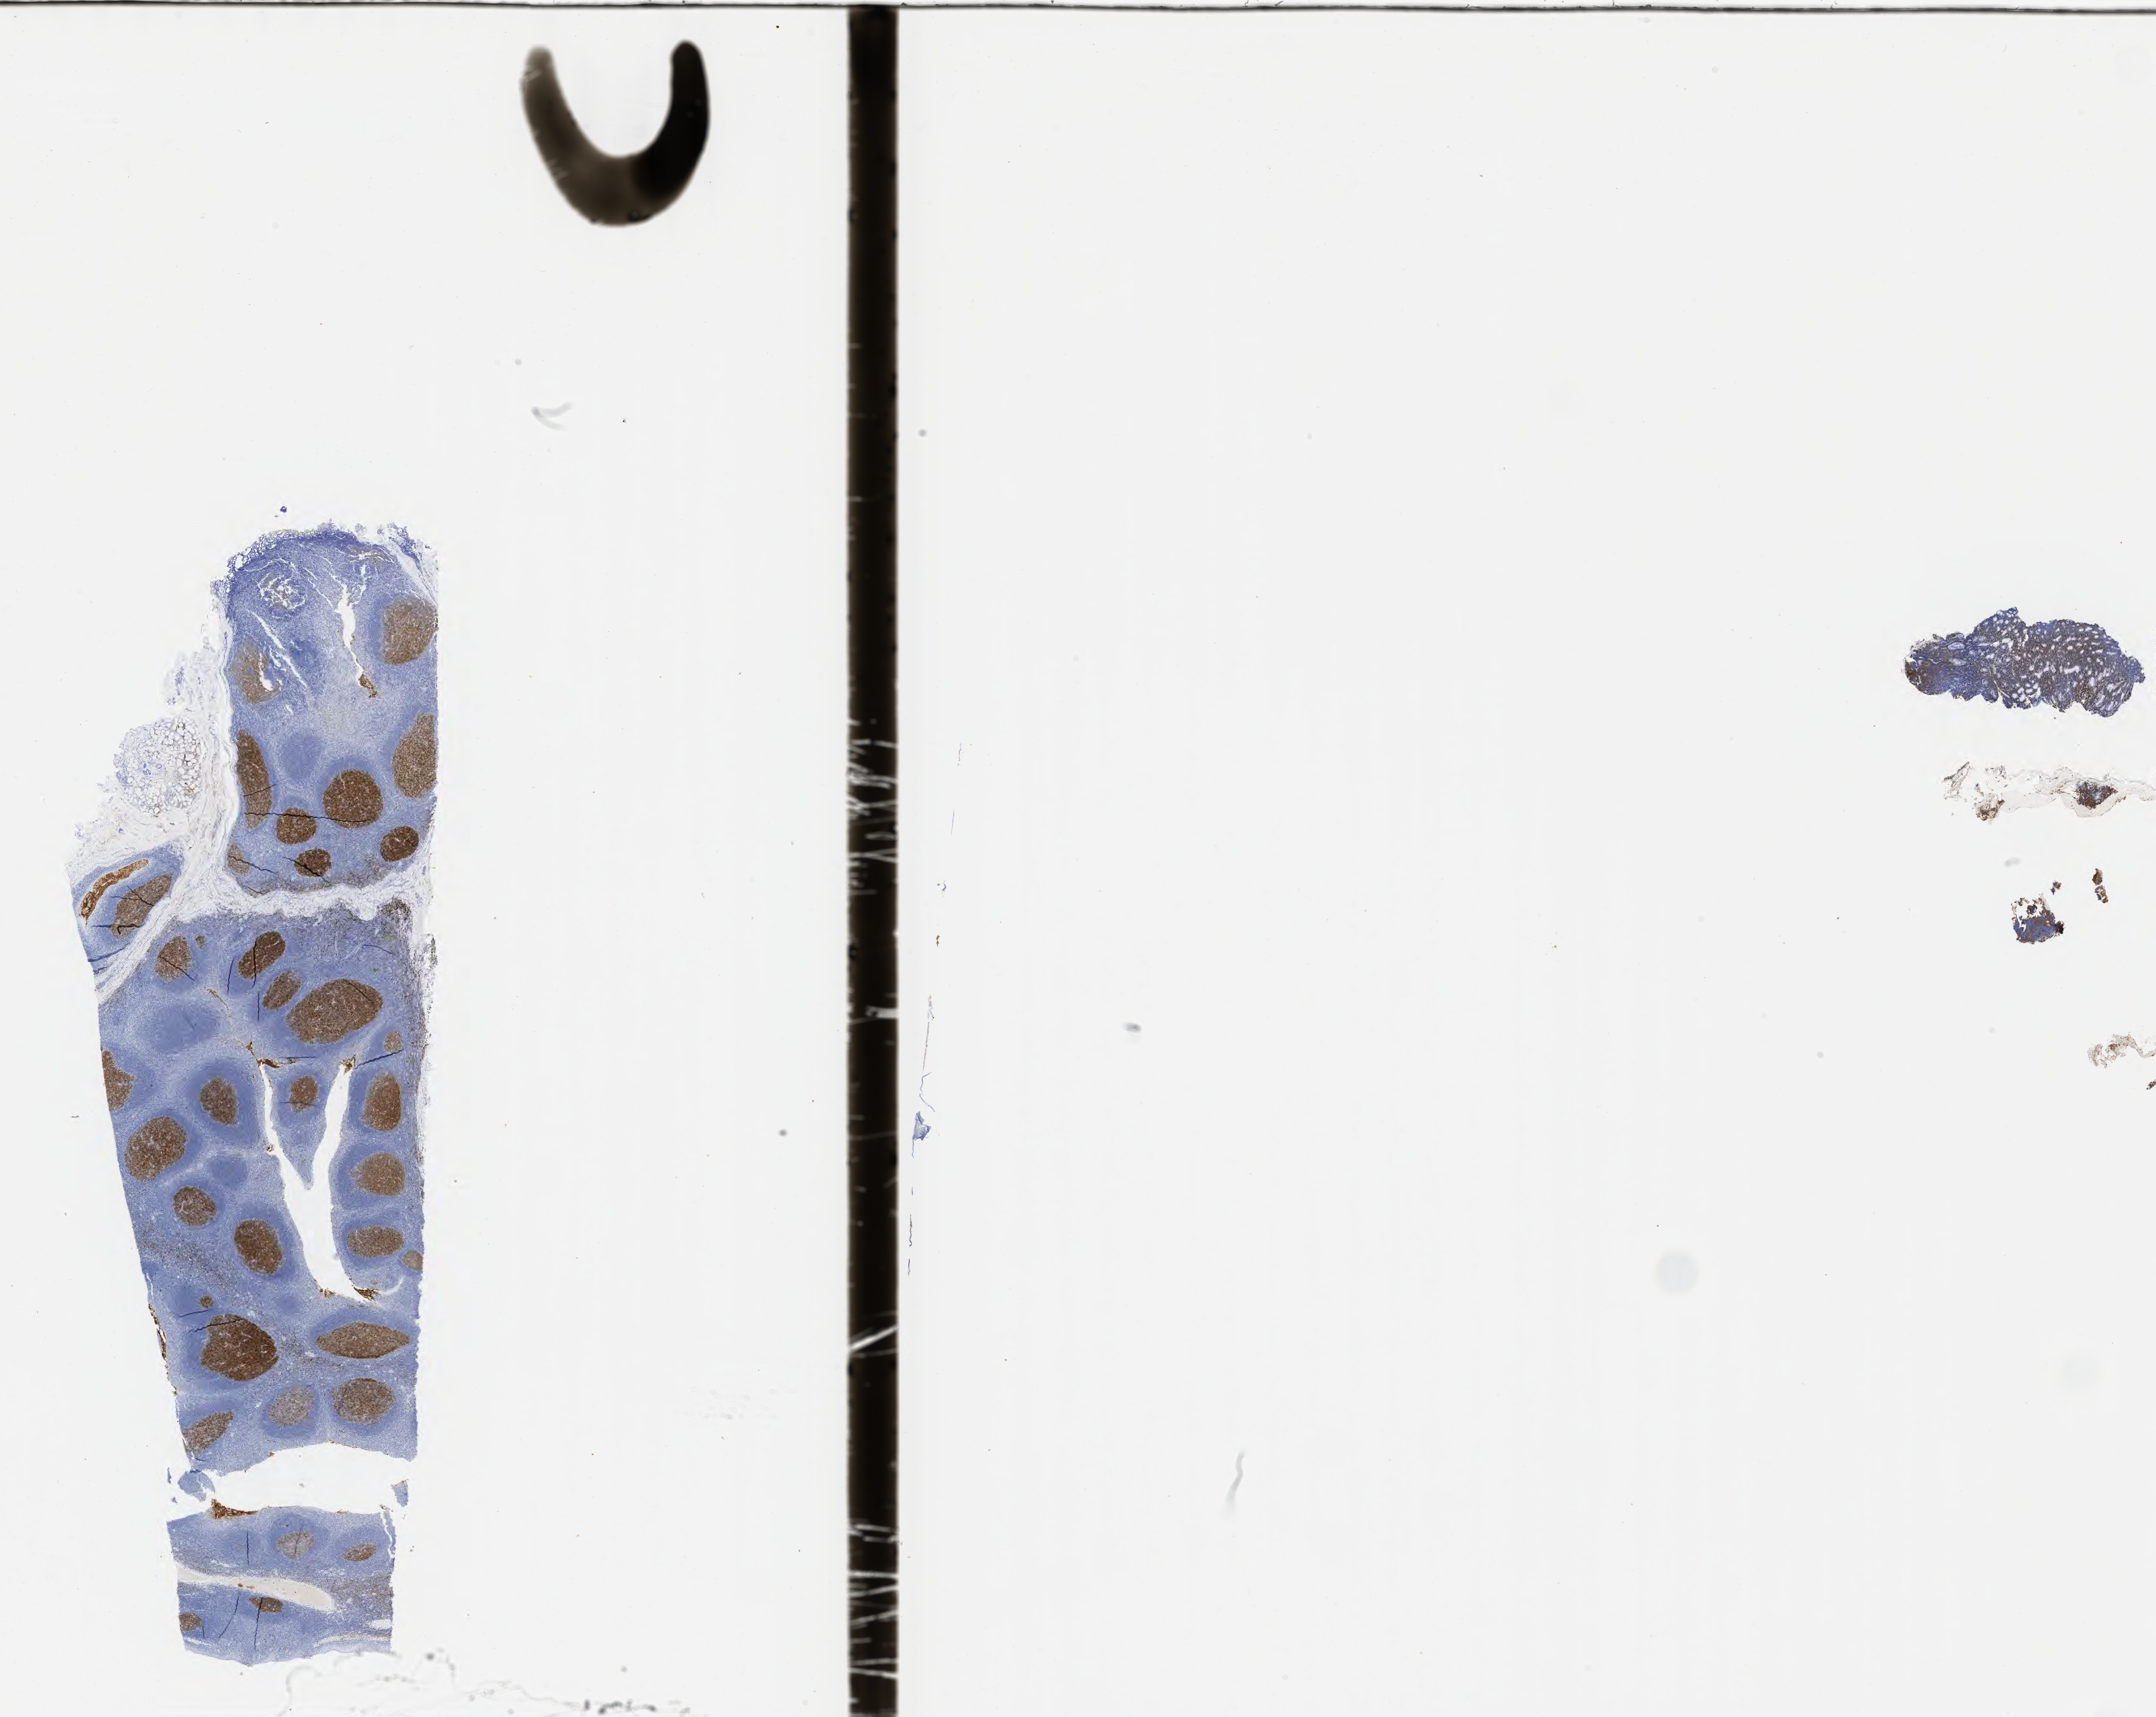
Immunohistochemistry (IHC) whole-slide image stained for CD10 — a low-resolution overview of the entire scanned area, about 26.7 x 21.3 mm; specimen: tumor tissue; anatomic site: stomach. Patient female; 28 years old.
Histologic diagnosis: Burkitt lymphoma, NOS.